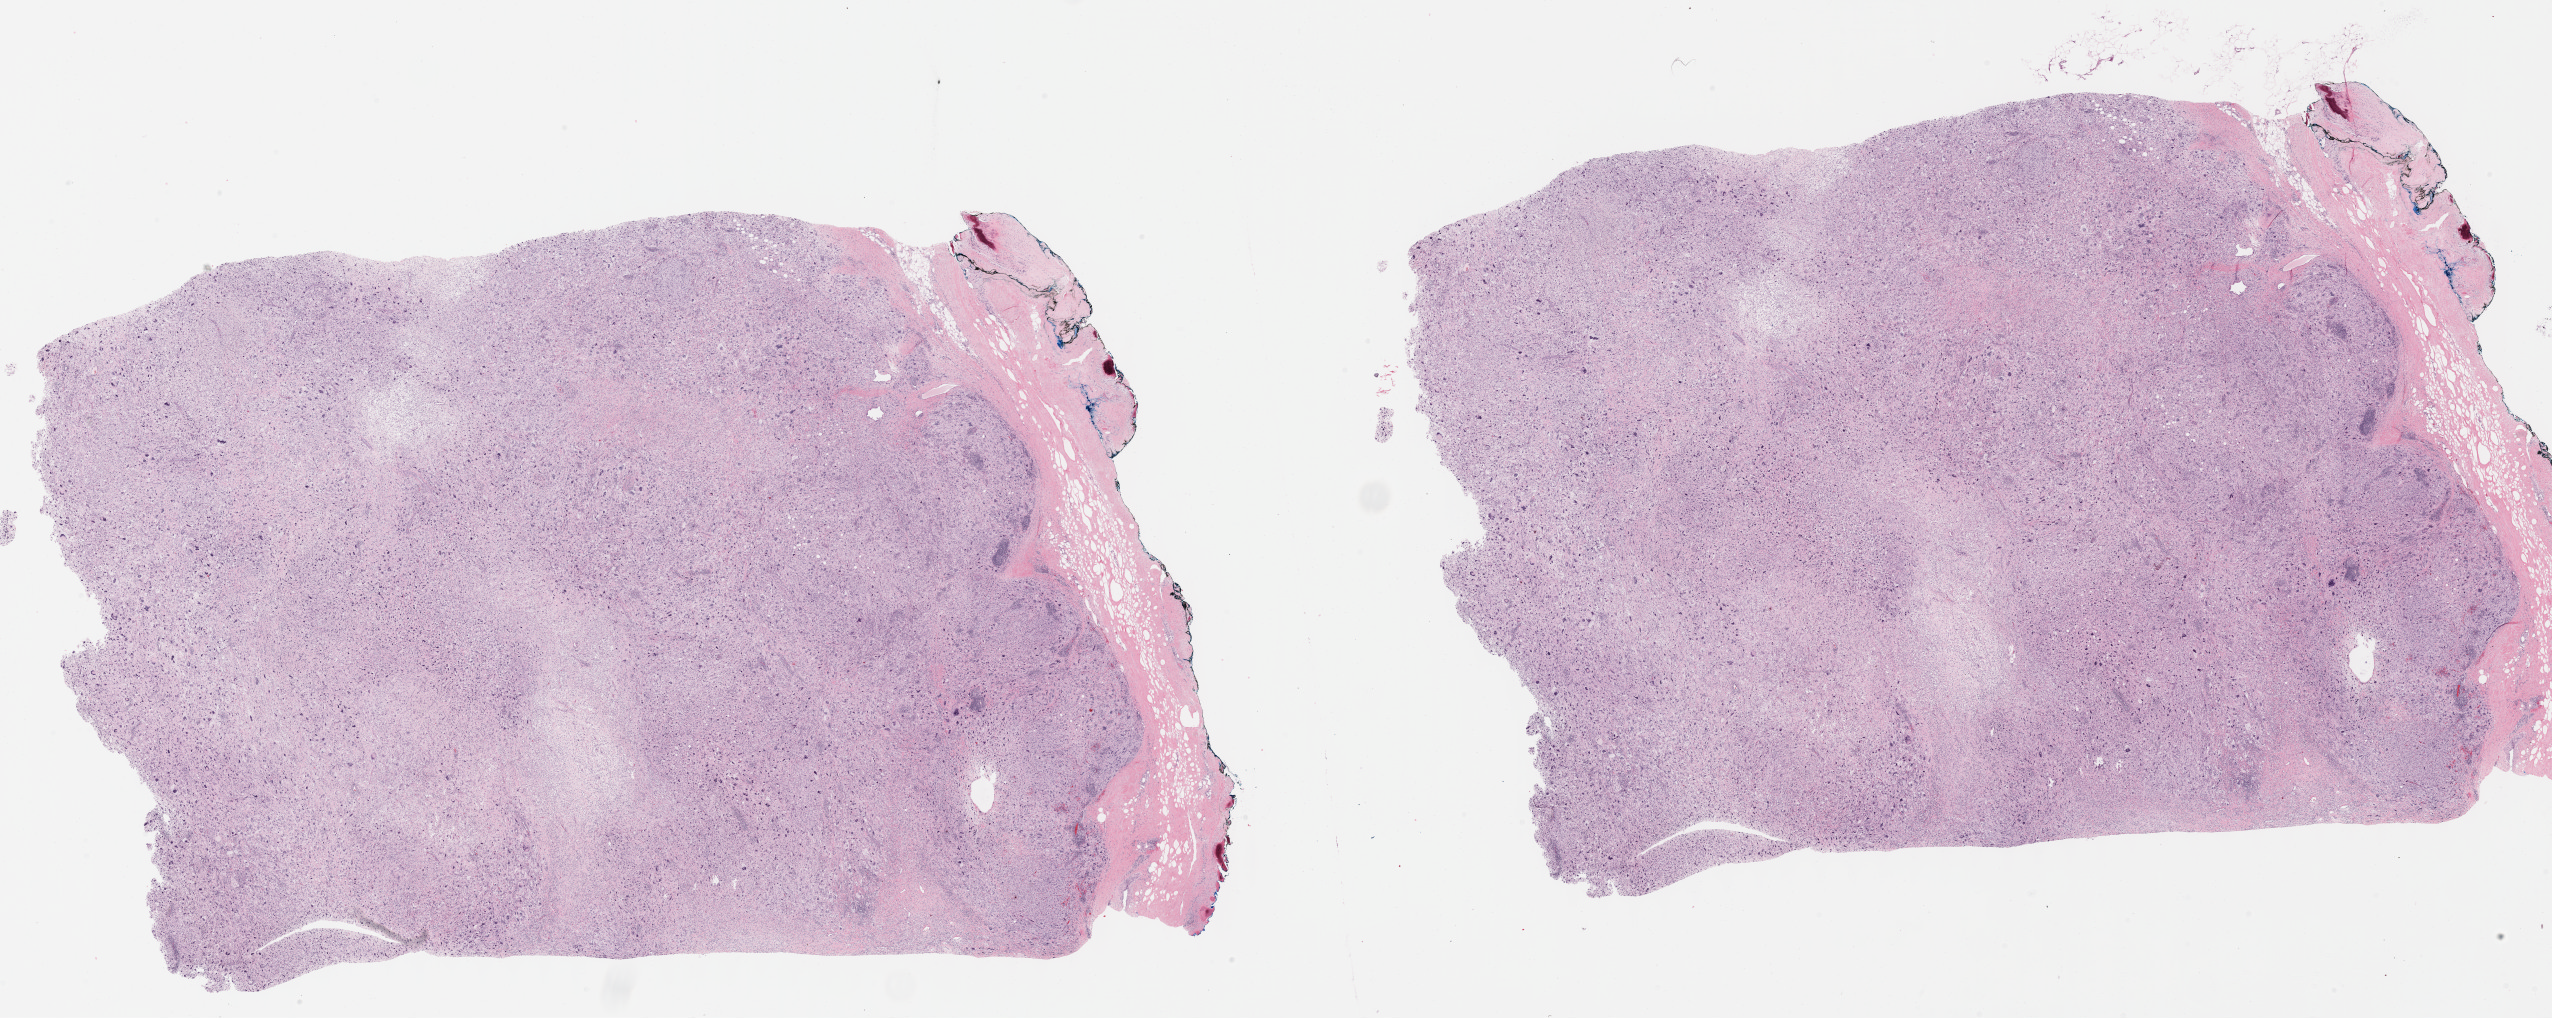
Digitized Hematoxylin and eosin (H&E) stained tissue section (whole slide) — a low-resolution overview of the entire scanned area, about 41.2 x 16.5 mm; formalin-fixed paraffin-embedded (FFPE) diagnostic section; connective, subcutaneous and other soft tissues, primary tumour sample. Patient: female, age at initial diagnosis 67 years.
• diagnosis: Undifferentiated sarcoma (connective, subcutaneous and other soft tissues of lower limb and hip)